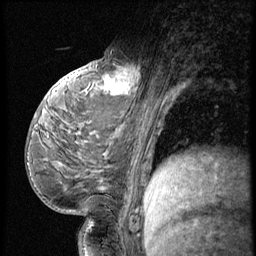
Breast MRI (dynamic contrast-enhanced), one sagittal slice. Slice 32 of 56 in the series (ordered by position). 3 images stored at this slice position (order not interpretable as contrast timing). 1.5 T. TE 4.2 ms, TR 9 ms. 2.5 mm slice thickness. 256 × 256 image matrix, field of view 180 × 180 mm. Female patient, age 54 years. Case-level facts recorded for this patient, not image findings: setting: breast cancer imaged before/during neoadjuvant chemotherapy; receptor status: triple-negative.
Outlined on this slice (semi-automatically segmented with operator editing):
- analysis volume of interest (the breast-tissue region the enhancement analysis was run in; not a lesion): box from (x=99, y=53) to (x=149, y=102) px
- tumour enhancement mask (voxels above the 140 % enhancement threshold inside the analysis volume of interest): (x=106, y=64)–(x=141, y=94)